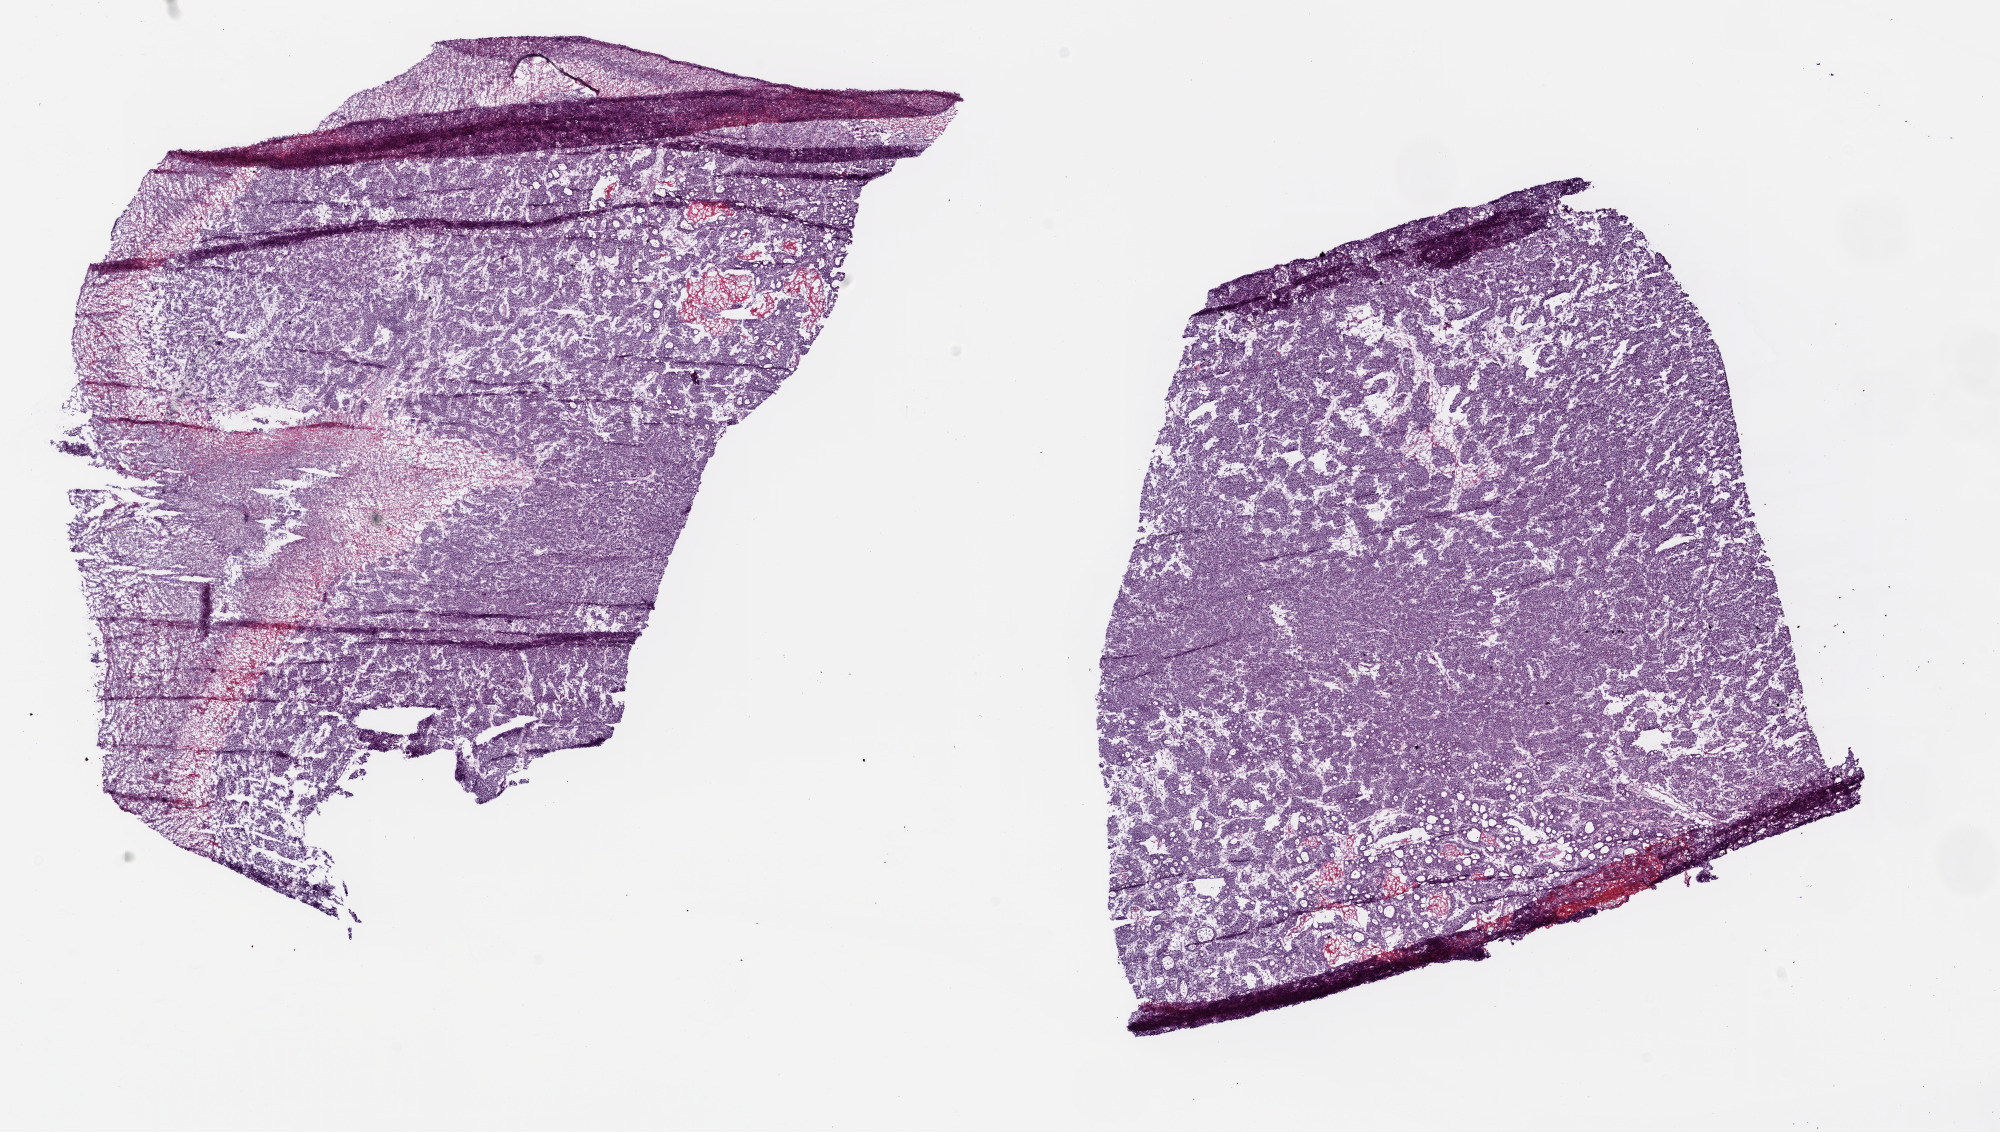
Whole-slide histology image, Hematoxylin and eosin (H&E) stained — shown as a low-resolution overview of the whole scanned area (about 16.0 x 9.1 mm), frozen section, primary tumour sample from the stomach. Male, age 70 years at initial diagnosis. Histologic grade: G3 (poorly differentiated). Pathologist review of this section (percent, as recorded): tumour cells 90%, tumour nuclei 75%, normal cells 0%, stromal cells 5%, necrosis 5%.
* lymph nodes positive (case pathology): 39 of 40 examined
* diagnosis: Adenocarcinoma, intestinal type
* AJCC pathologic stage: IV (6th edition)